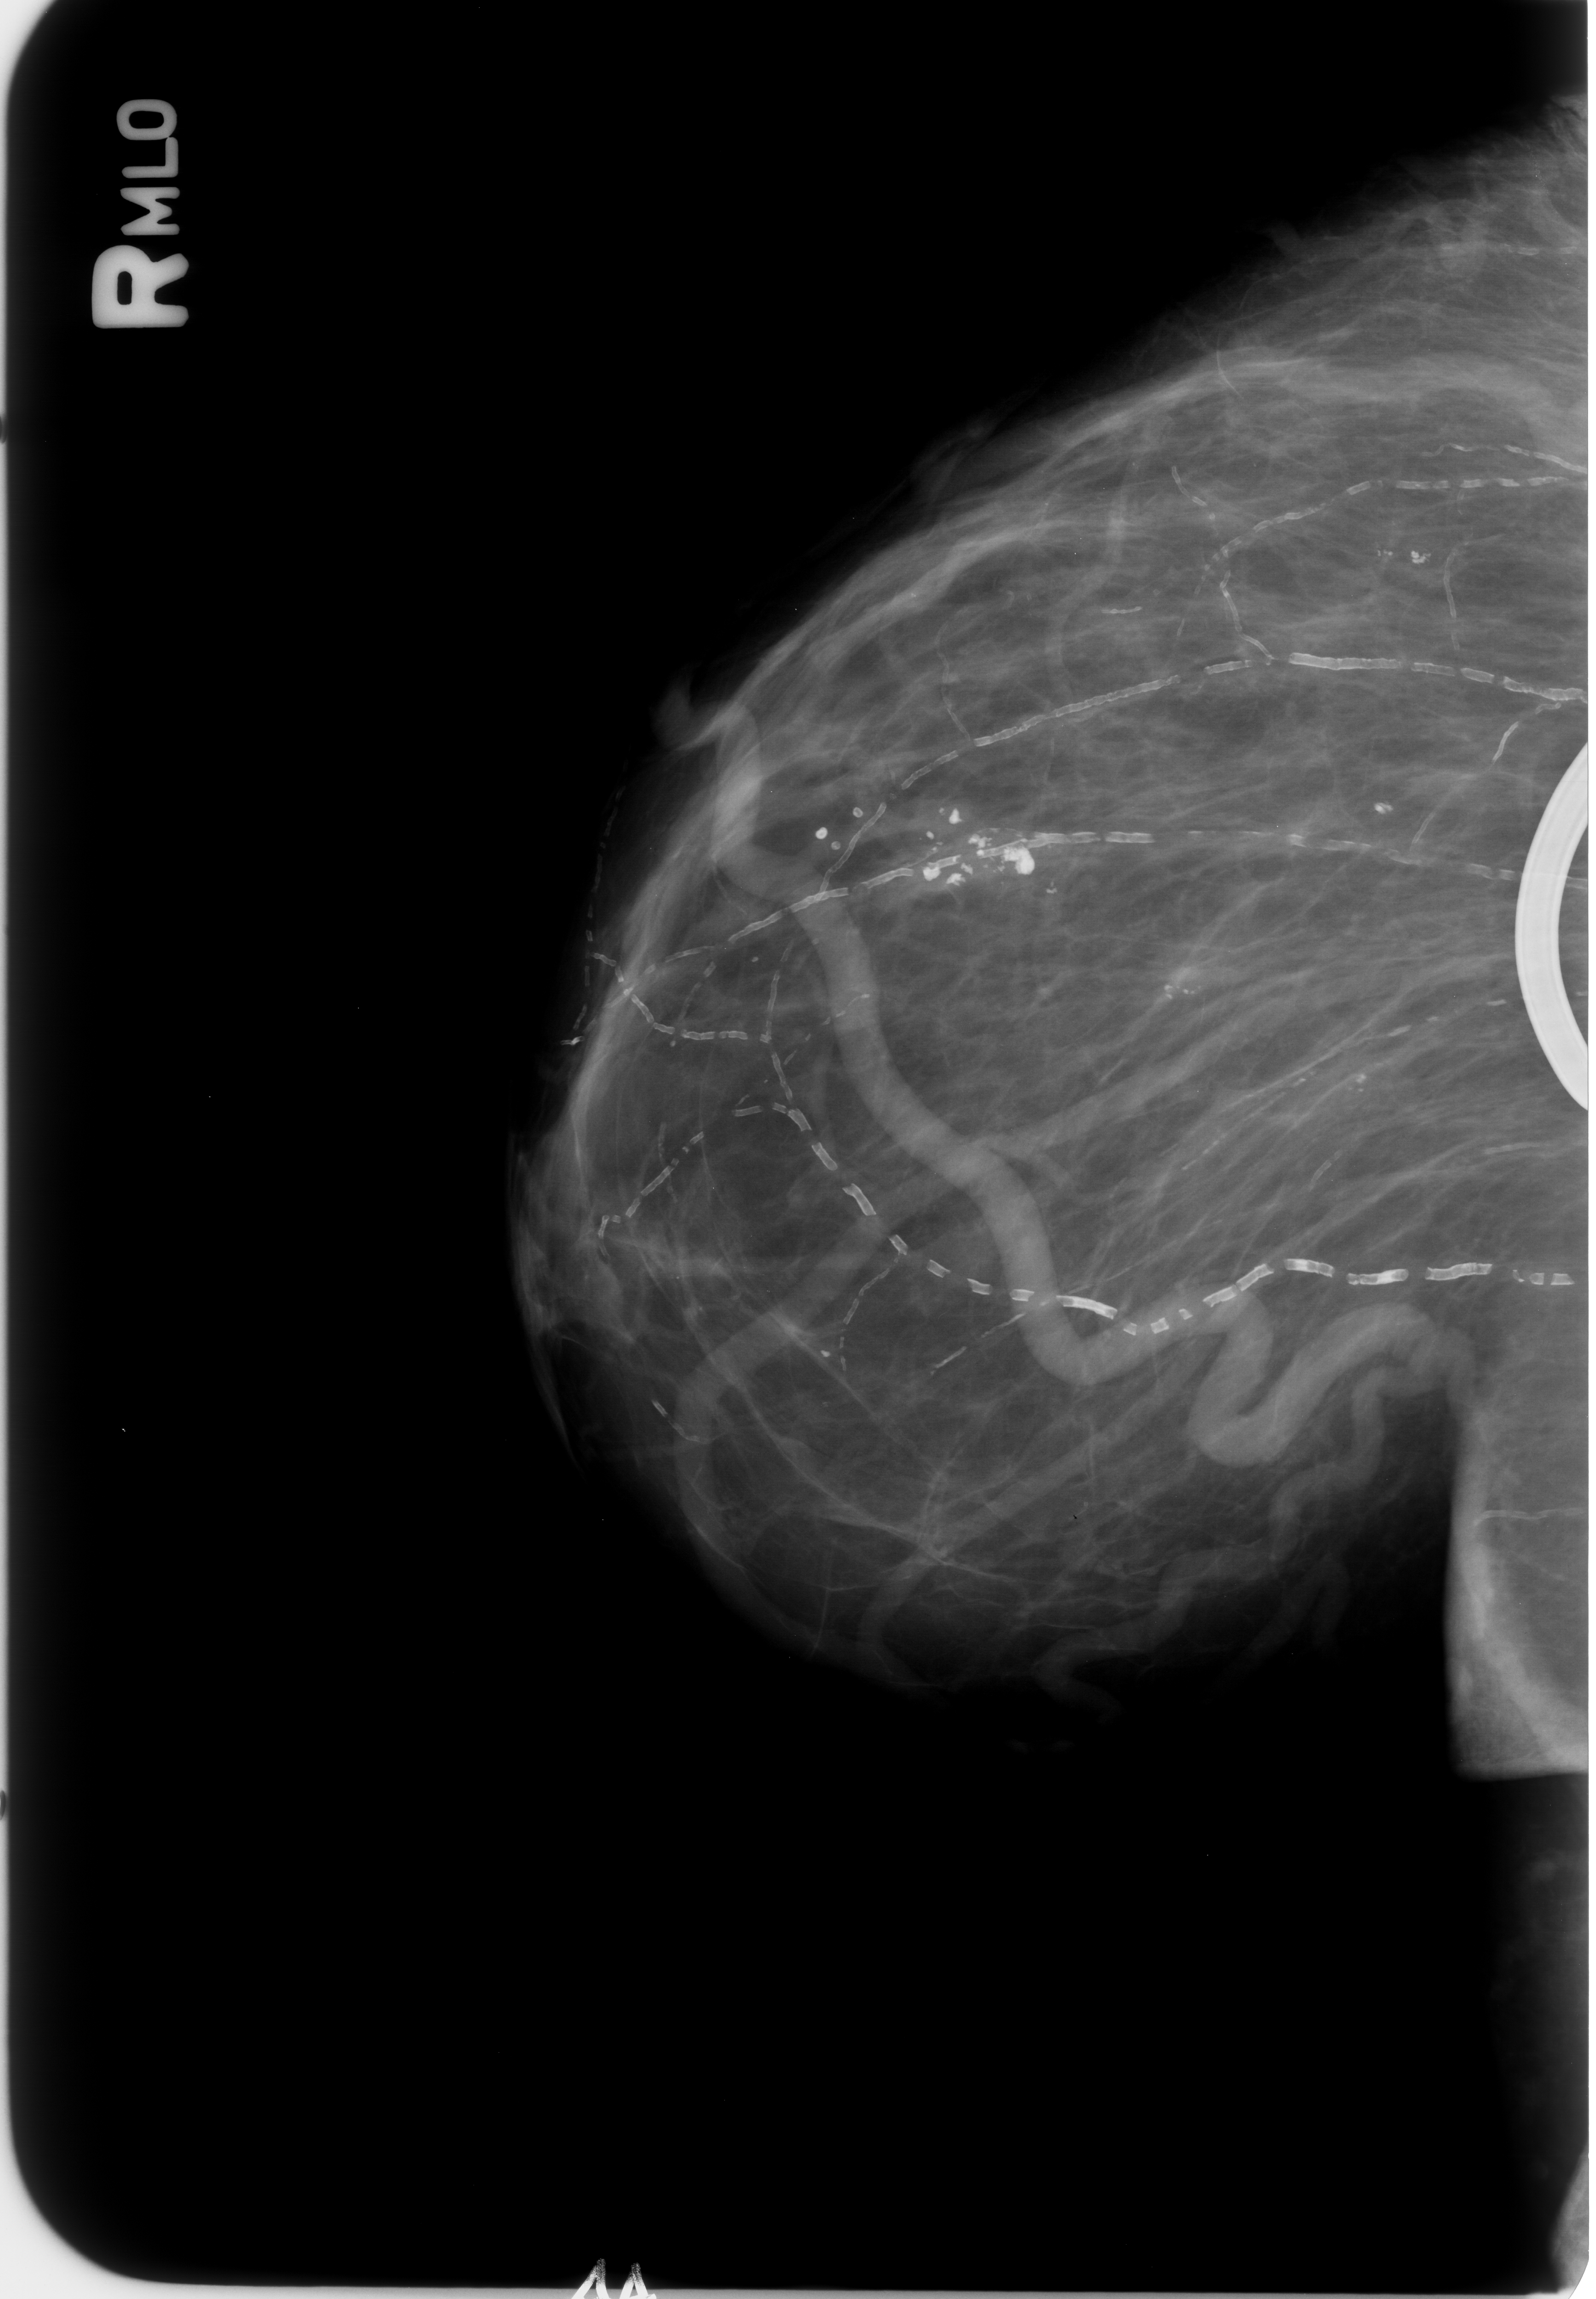
Scanned film-screen mammogram; right breast; MLO view; breast composition: almost entirely fatty (BI-RADS density category 1 of 4).
Finding: calcifications, morphology coarse / pleomorphic, distribution clustered; BI-RADS assessment category 2; pathology (as recorded): benign.